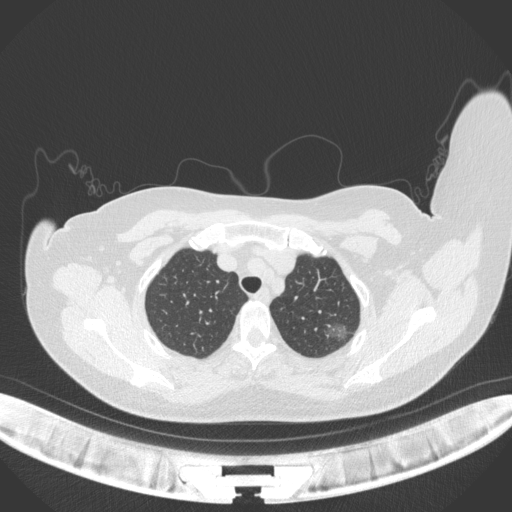
Chest CT, one axial slice. Slice 308 of 386 in the series (ordered by position). 120 kVp. Lung window (W 1500 / L -600 HU). 1 mm slice thickness. 512 × 512 image matrix, field of view 400 × 400 mm. Patient: female, 58 years. From the clinical record (not read from this slice): clinical TNM (as recorded): T1c N0 M0.
Annotated regions visible in this slice (rectangle marked by the reading radiologist):
- lung tumour (recorded histology: adenocarcinoma): bounding box [x1, y1, x2, y2] px = [323, 318, 352, 342]